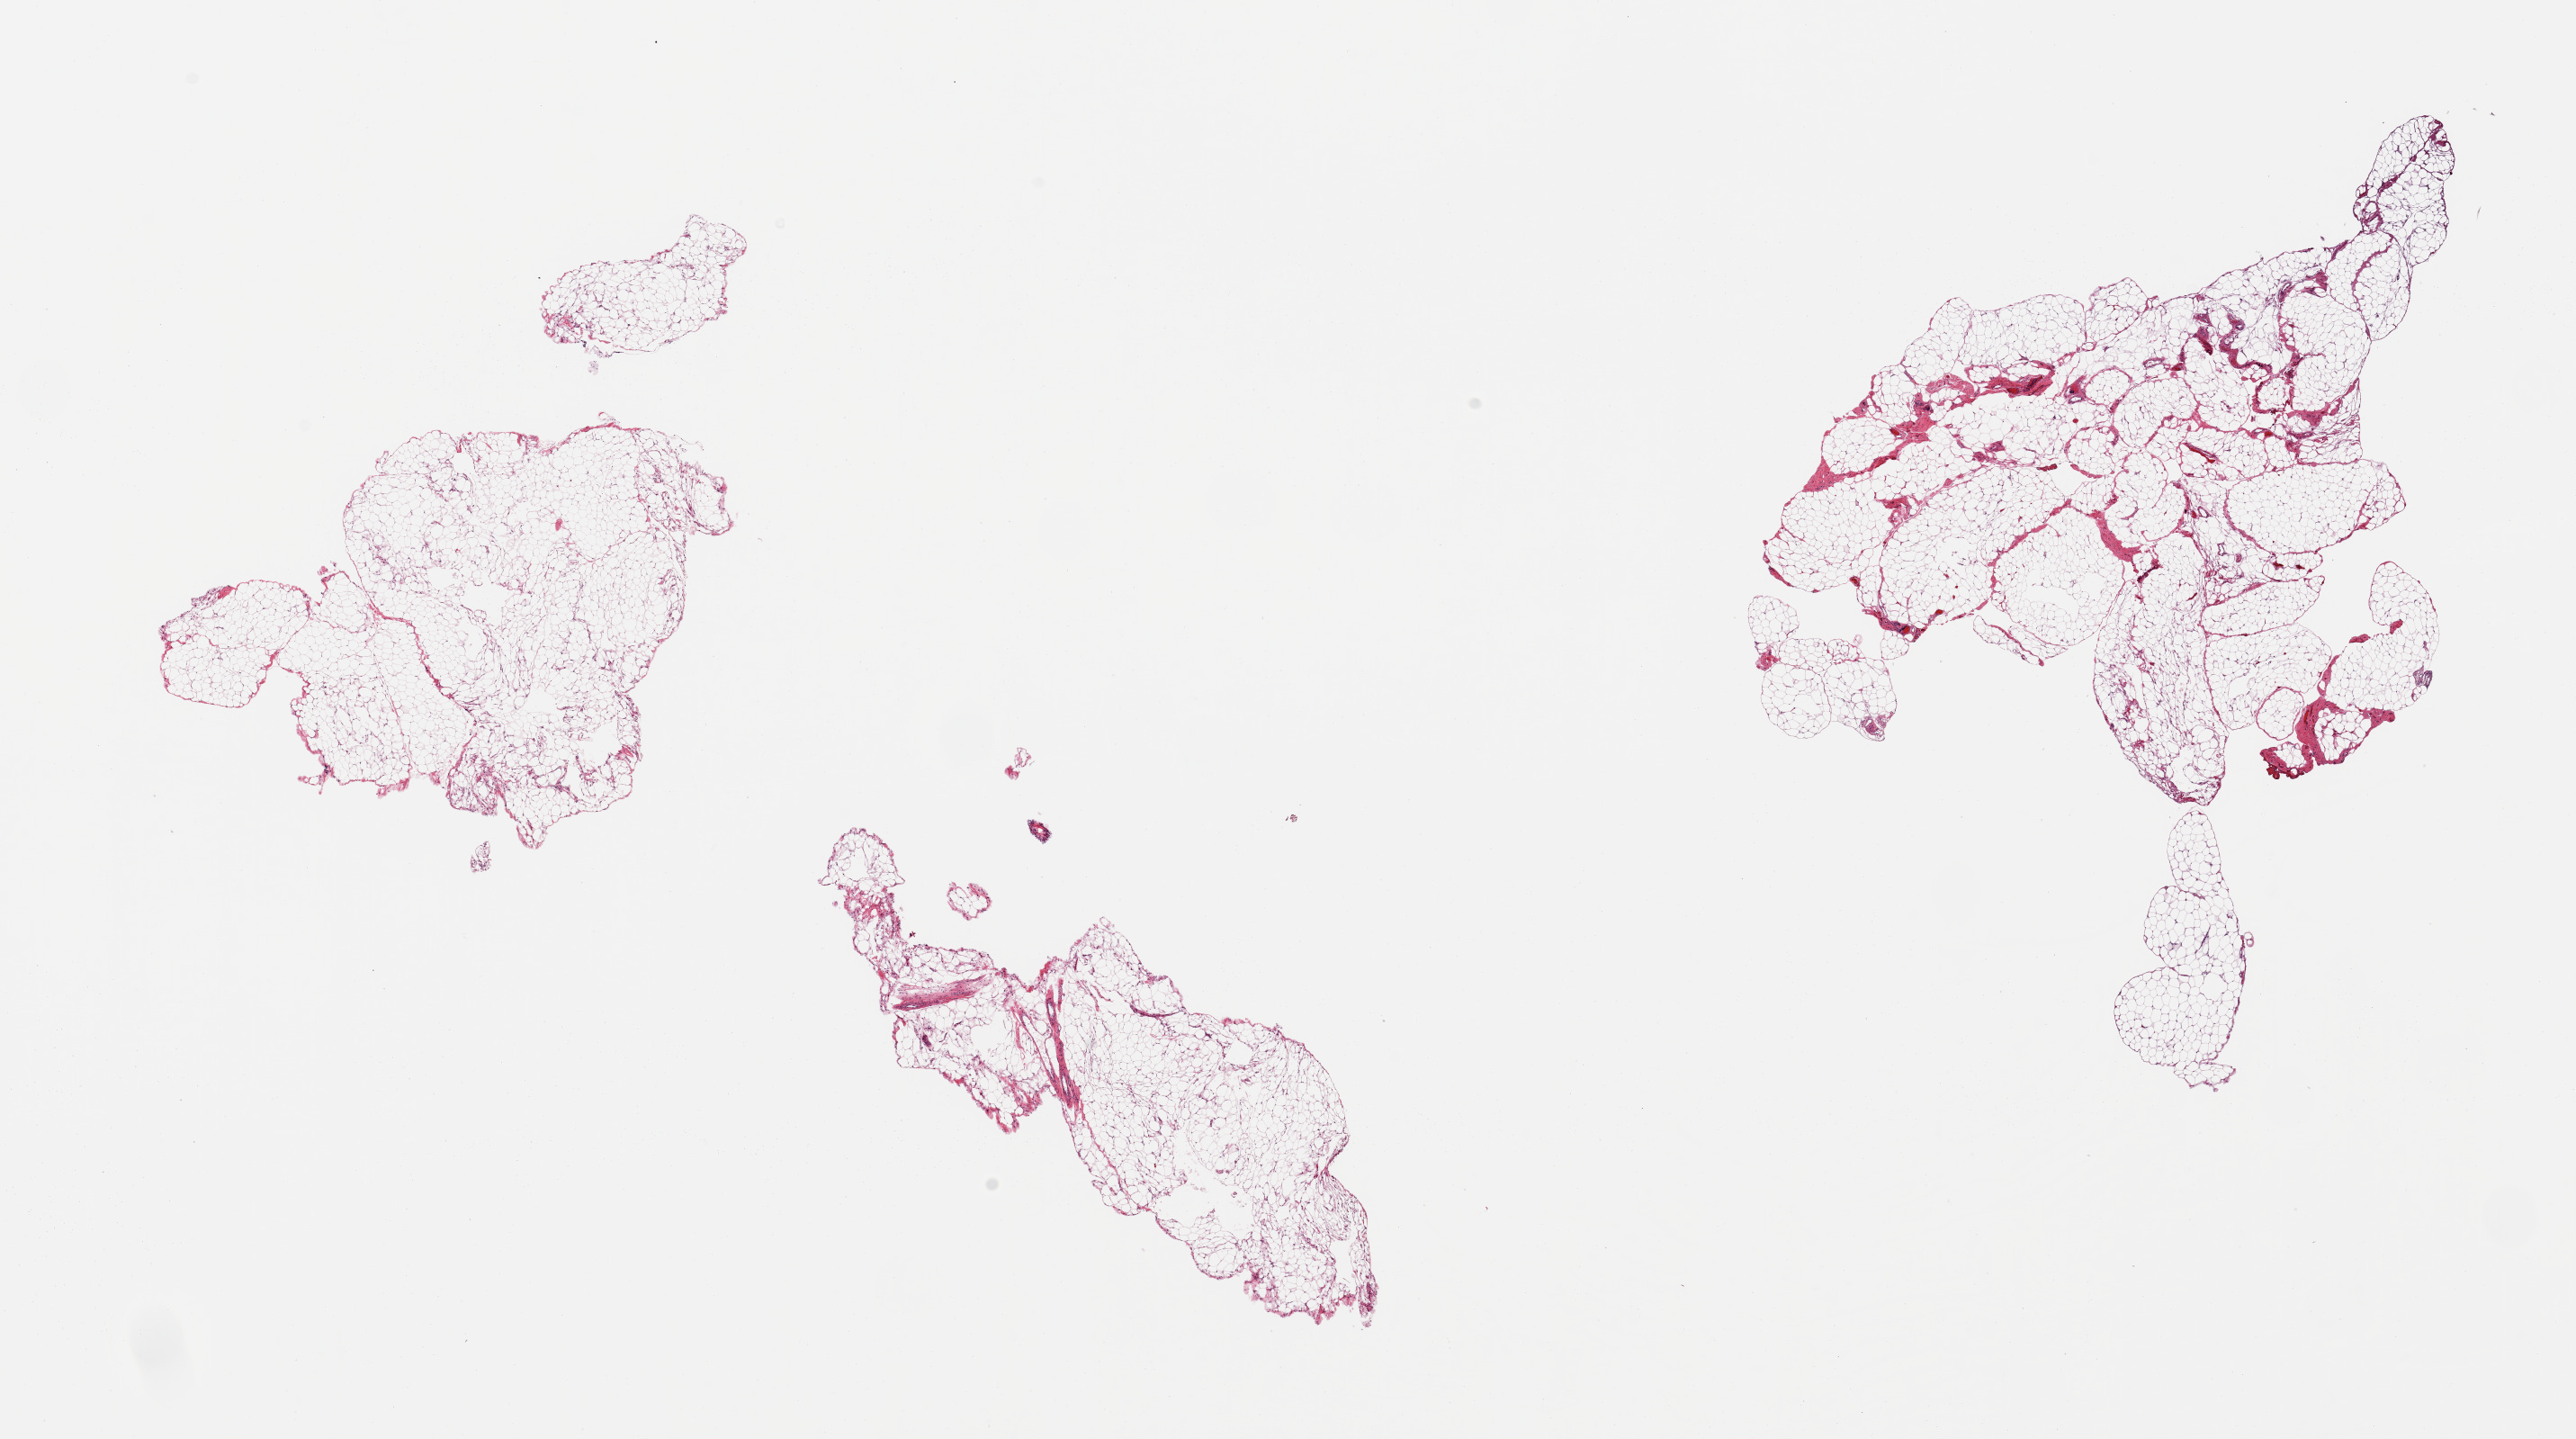
Digitized haematoxylin and eosin-stained section, brightfield — a low-resolution overview of the entire scanned area, about 22.6 x 12.6 mm; PAXgene-fixed paraffin-embedded (PFPE) section; section of omentum (target tissue); tissue donor sample. Donor: male.
• pathologist's review note for this sample: 2 pieces